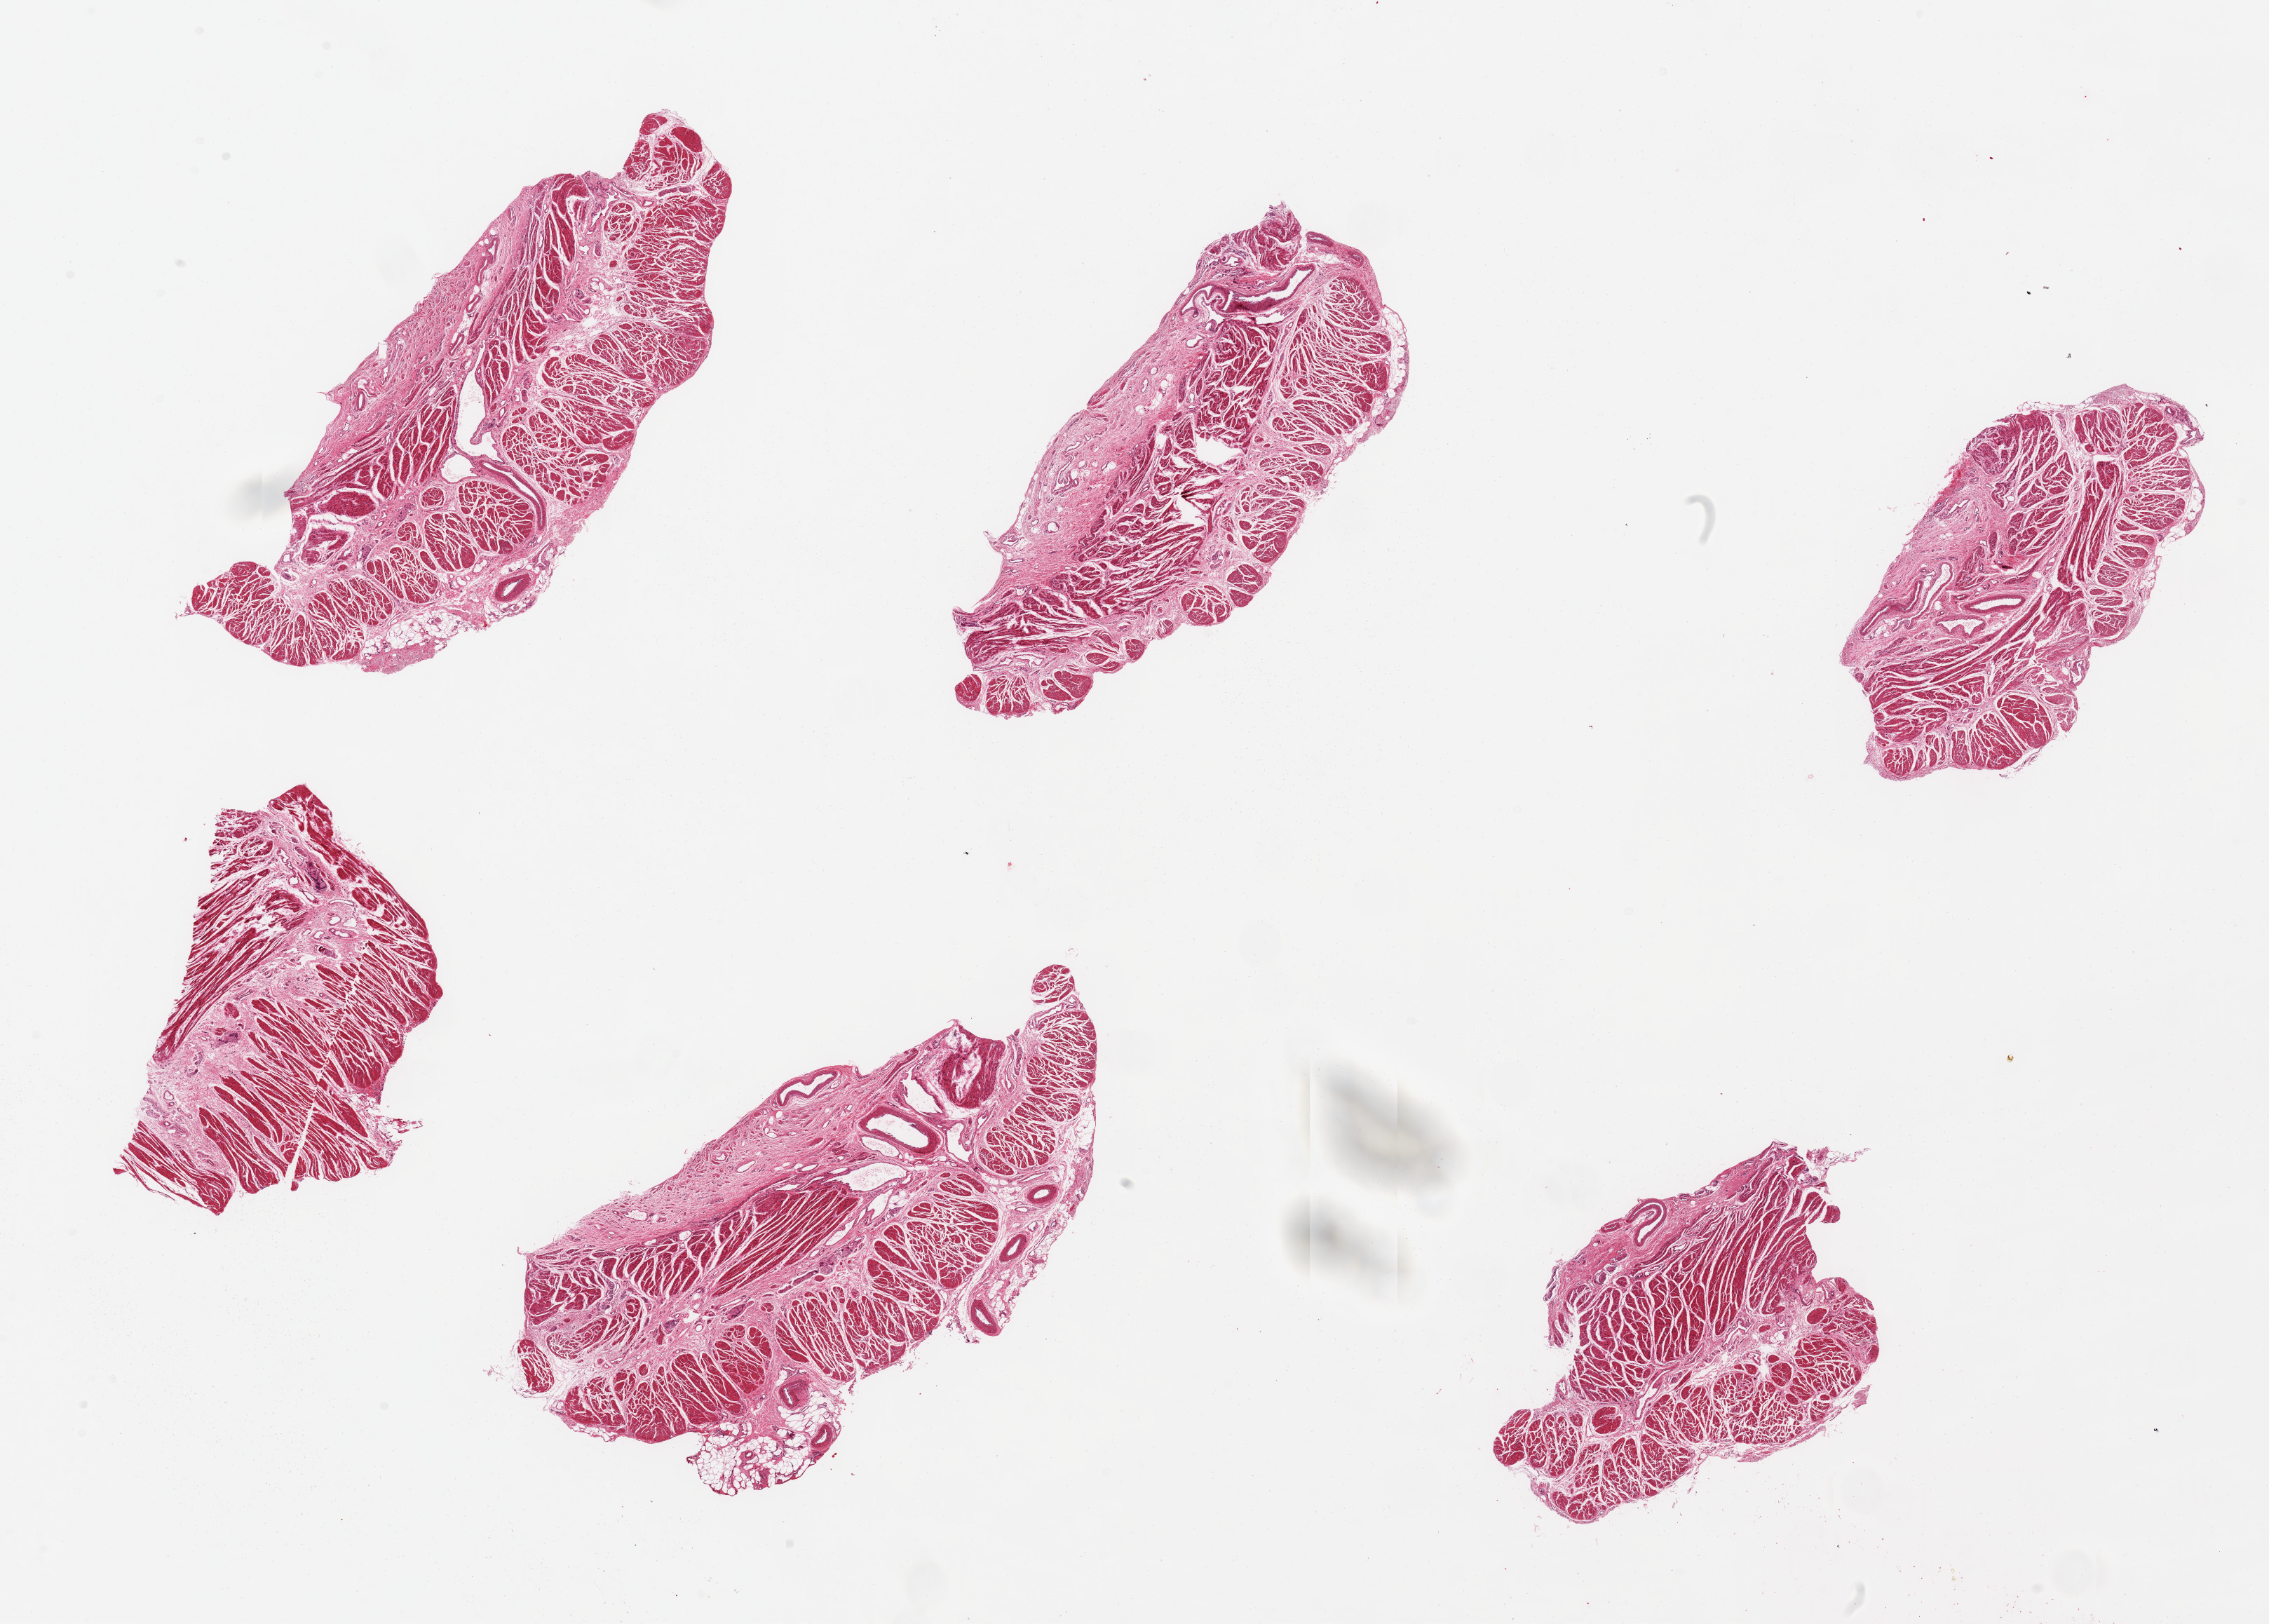
H&E whole-slide image, shown as a low-resolution overview of the whole scanned area (about 25.6 x 18.3 mm, slide scanned at 20x), PAXgene-fixed paraffin-embedded (PFPE) section, target tissue: gastroesophageal junction, tissue donor sample. Male donor.
Pathologist's review note for this sample: 6 pieces; target muscularis, small attachments of submucosa/adventitia.